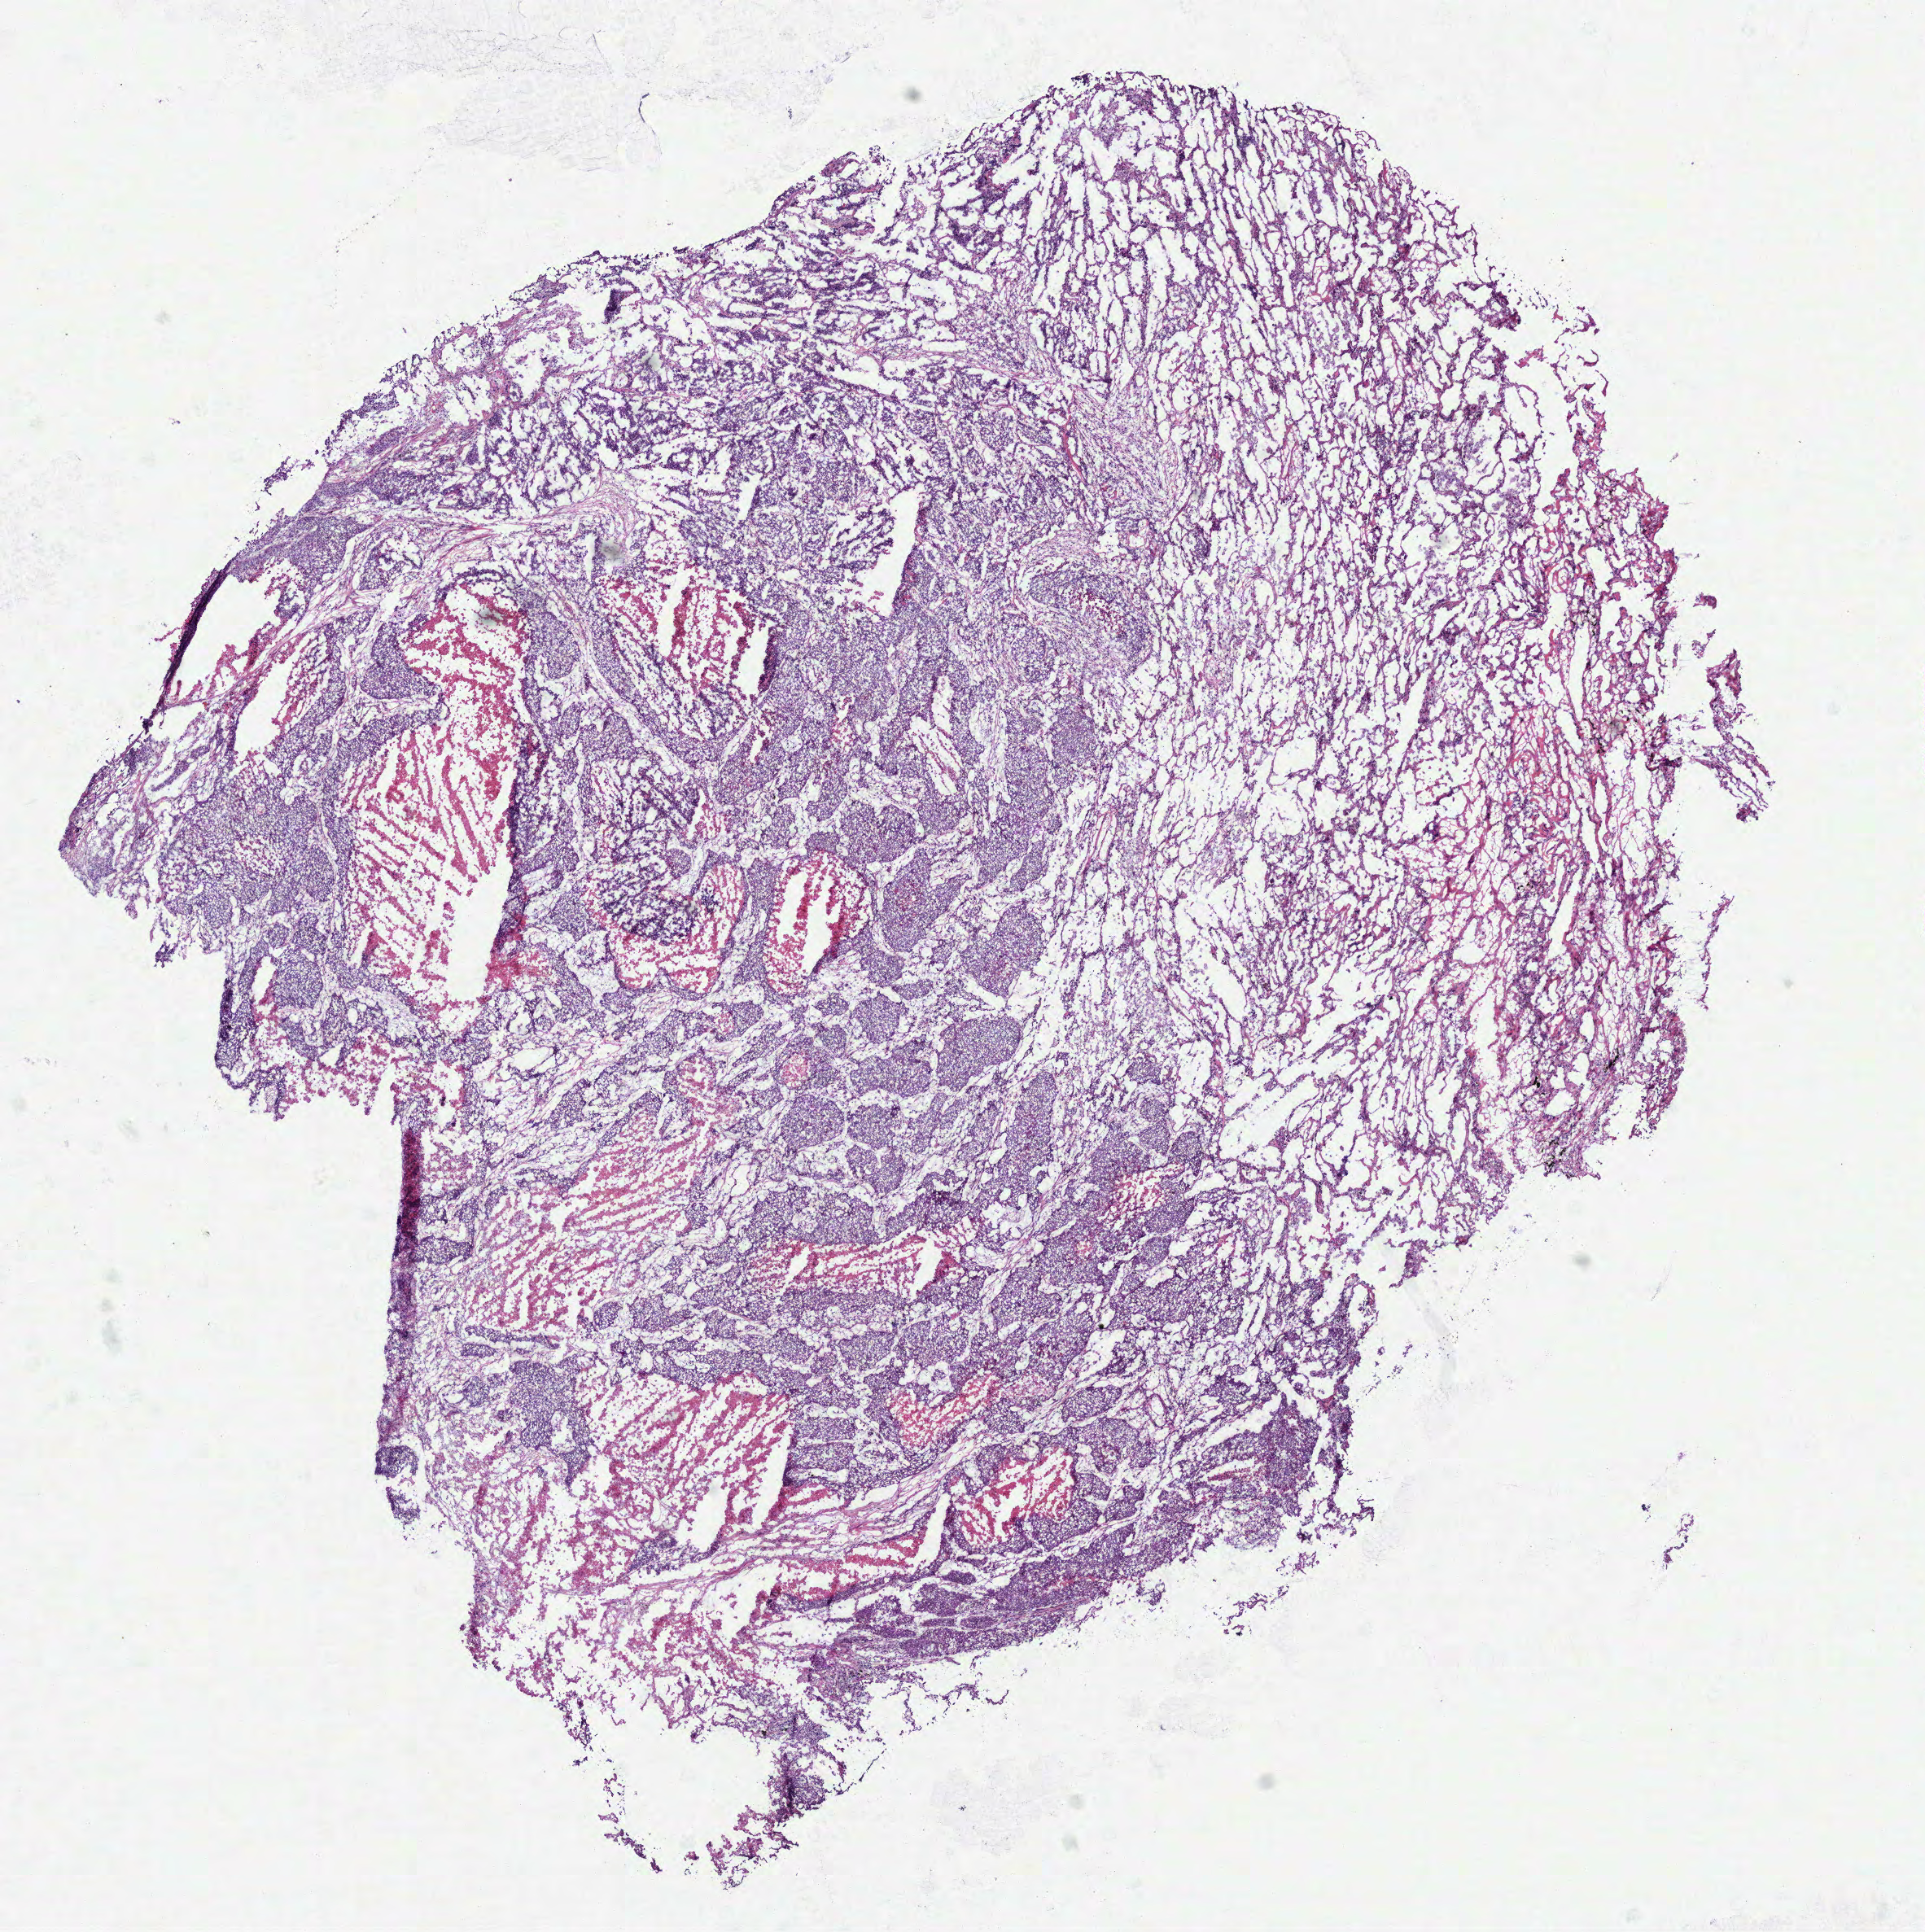
Digitized Hematoxylin and eosin (H&E) stained tissue section (whole slide) — a low-resolution overview of the entire scanned area, about 9.5 x 9.6 mm (from a 40x scan). Frozen section from the top of the tissue portion. Lung, primary tumour sample. Patient: female, age at initial diagnosis 70 years. Slide review estimates, as recorded: tumour cells 54%, tumour nuclei 70%, normal cells 32%, stromal cells 0%, necrosis 14%. Inflammatory infiltration, as recorded: lymphocyte infiltration 2%, monocyte infiltration 10%, neutrophil infiltration 0%.
- laterality: right
- AJCC pathologic stage: IA
- diagnosis: Squamous cell carcinoma, NOS (lower lobe, lung)